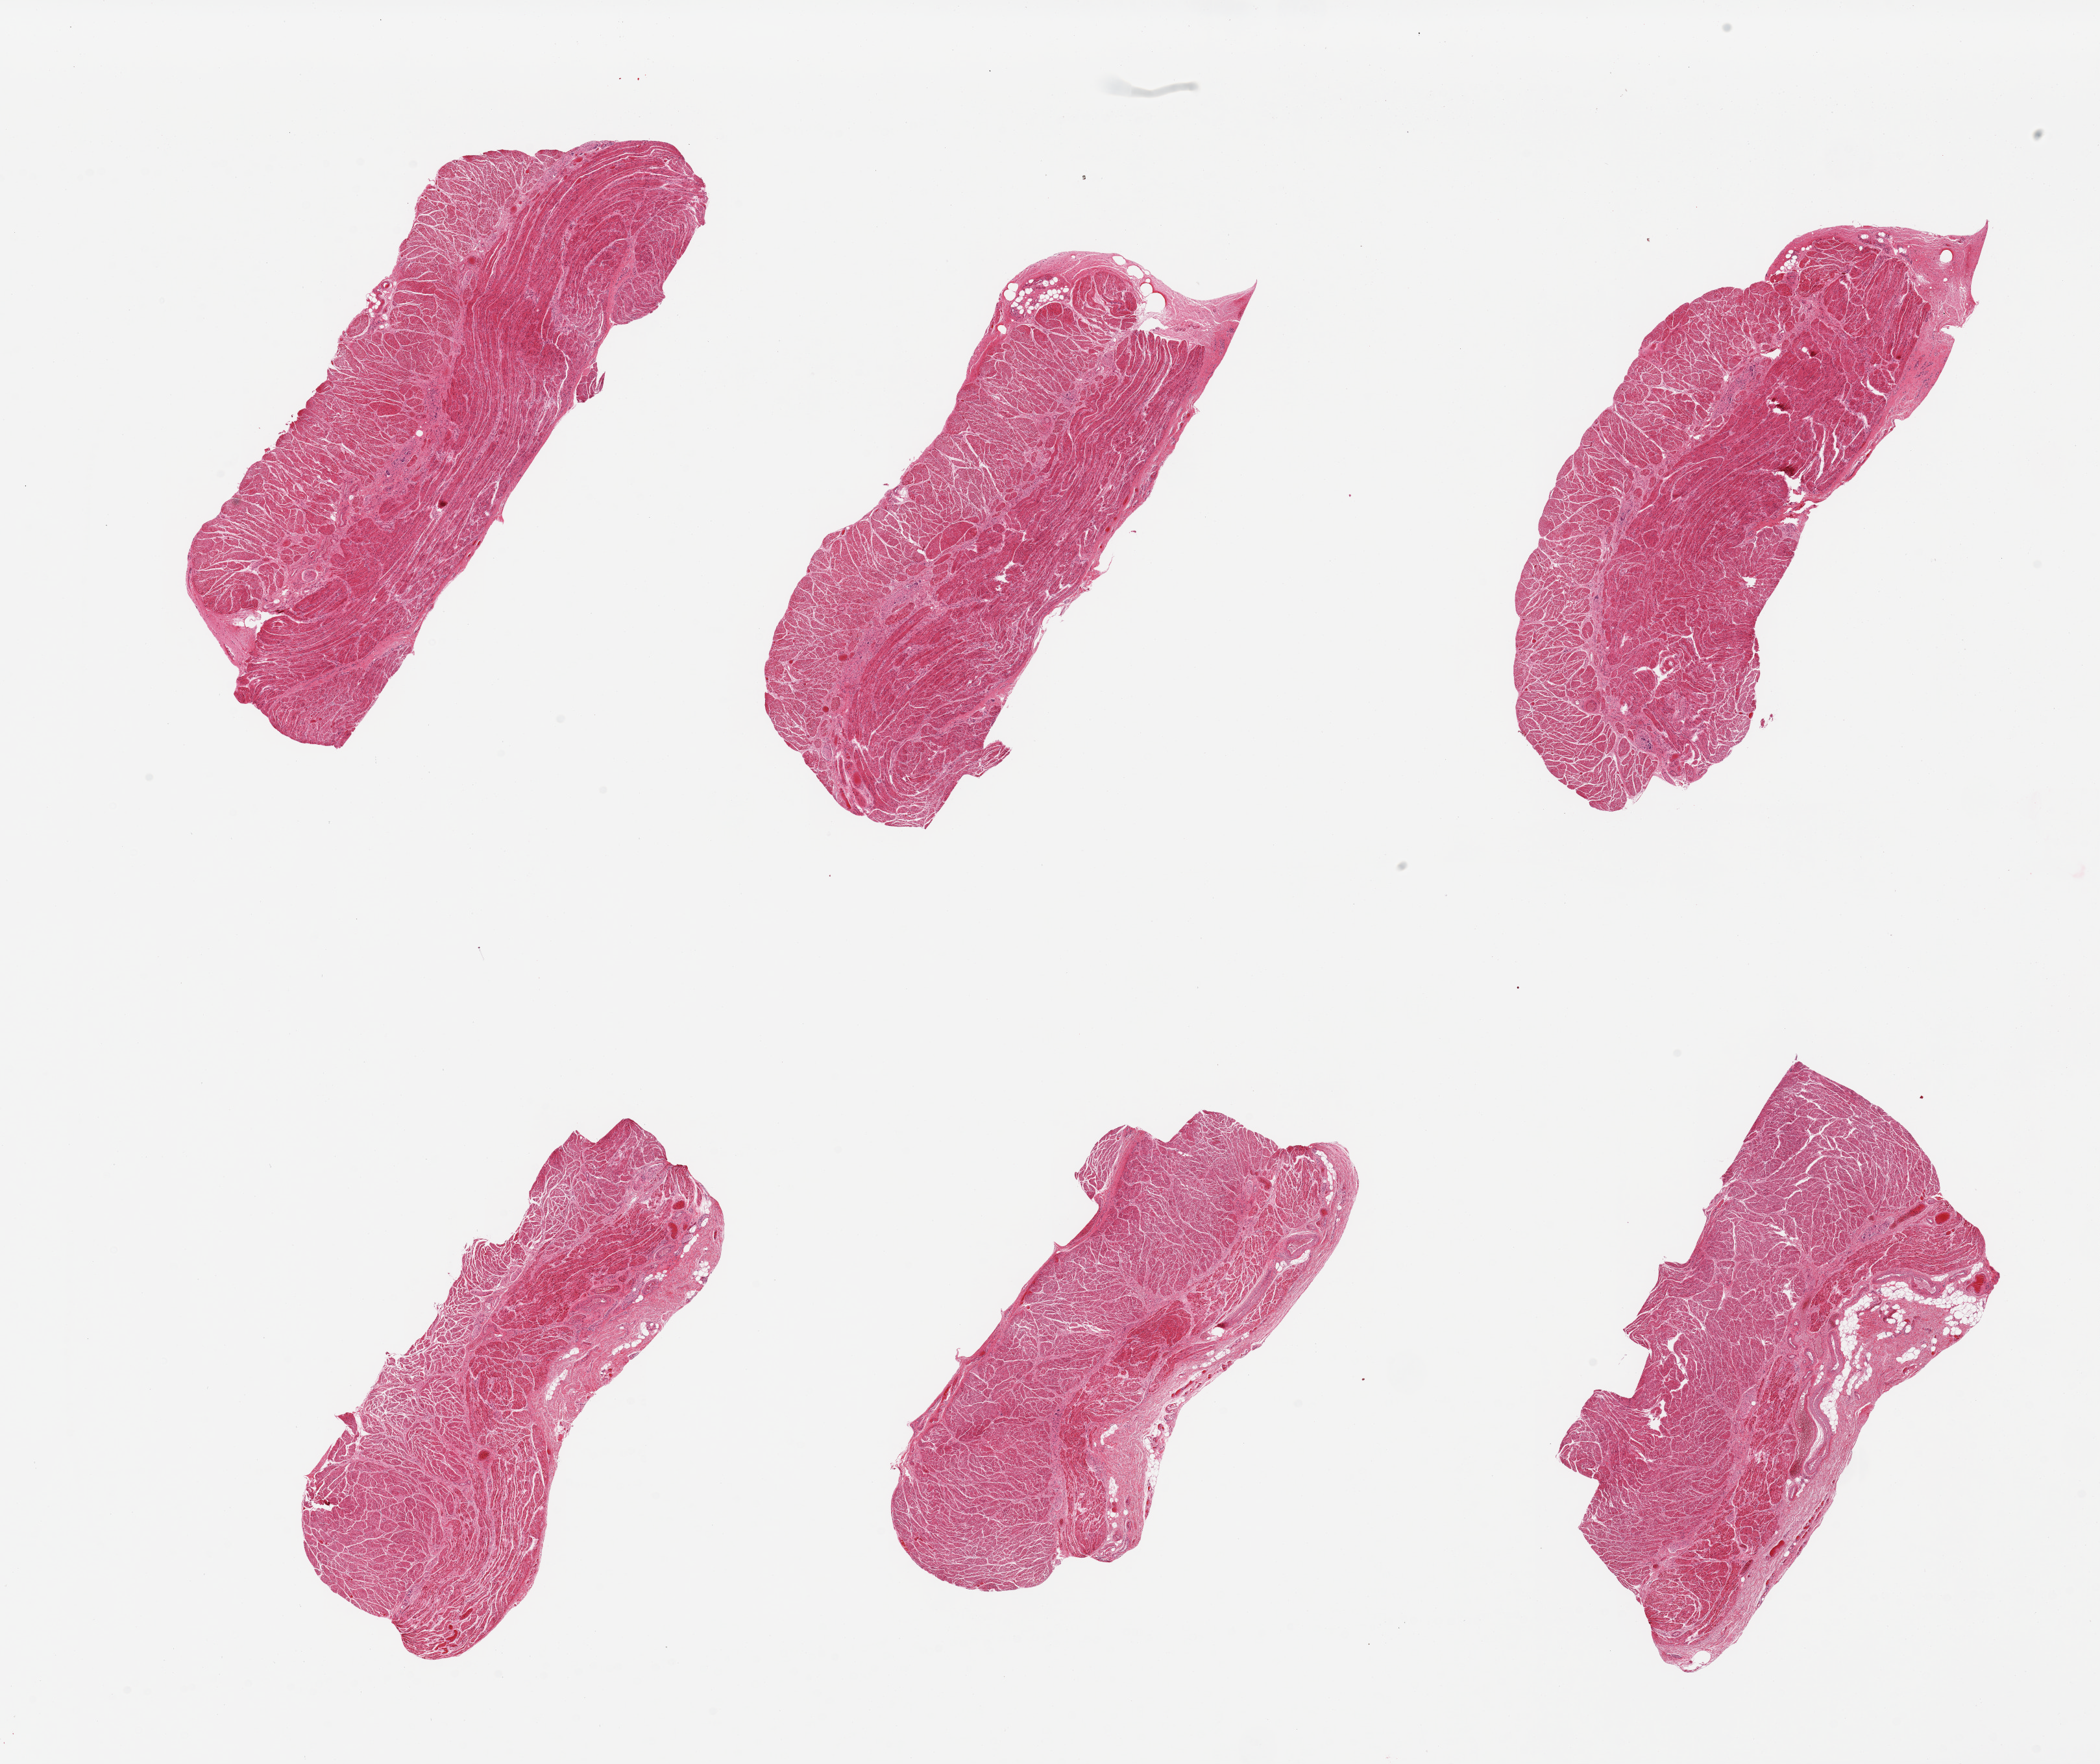
Haematoxylin and eosin whole-slide image — low-resolution overview of the scanned area, about 25.6 x 21.5 mm (slide scanned at 20x), PAXgene-fixed paraffin-embedded (PFPE) section, target tissue: gastroesophageal junction, donor tissue sample. Donor: male.
Reviewer comment on this tissue sample: 6 pieces. Well dissected.